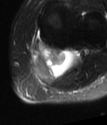
MRI of an extremity soft-tissue mass, one axial slice. Position 49 of 78 along the scan axis. T2-weighted fat-saturated. MR volume resampled by the dataset authors to the PET/CT grid (not the native acquisition matrix). 3.27 mm slice thickness. 107 × 125 image matrix, field of view 104 × 122 mm. Female patient. From the clinical record (not read from this slice): histological type: extraskeletal high grade osteogenic sarcoma; grade: high; site of the primary tumour: left calf.
Structures marked on this image (expert contour drawn on MRI and transferred to this co-registered scan by the dataset authors):
- gross tumour volume (mass): bounding box (x1, y1, x2, y2) in pixels: (30, 45, 77, 82)